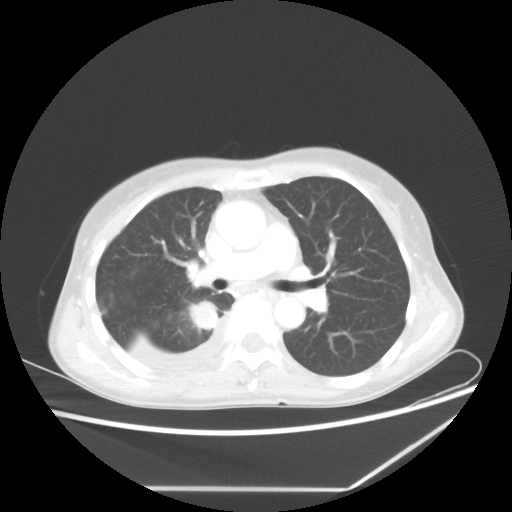
Chest CT, one axial slice. Position 35 of 60 along the scan axis. Reconstruction kernel STANDARD. 80 kVp. Lung window (W 1500 / L -600 HU). 5 mm slice thickness. 512 × 512 image matrix, field of view 364 × 364 mm. Patient: female, 59 years. Case-level facts recorded for this patient, not image findings: clinical TNM (as recorded): T1c N1 M1.
Outlined on this slice (rectangle marked by the reading radiologist):
- lung tumour (recorded histology: adenocarcinoma): bounding box [x1, y1, x2, y2] px = [189, 298, 220, 333]